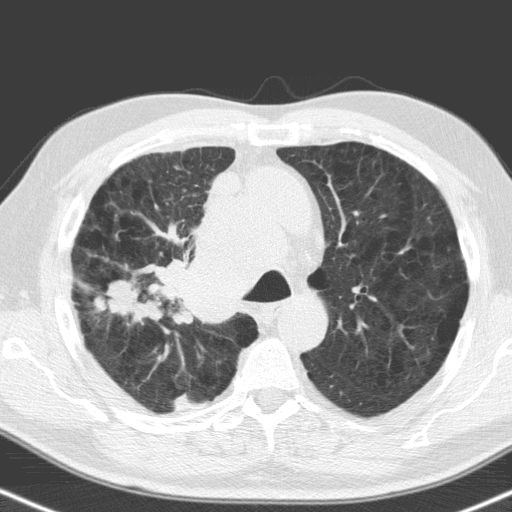
Low-dose screening chest CT, one axial slice; position 116 of 160 along the scan axis; lung window (W 1500 / L -600 HU); 3.2 mm slice thickness; 512 × 512 image matrix, field of view 324 × 324 mm.
Structures marked on this image (outlined manually by an expert reader):
- lesion 1 (tumor, hilum of right lung): bounding box <162,202,248,323> (left, top, right, bottom; pixels)
- lesion 2 (tumor, upper lobe of right lung): <108,281,152,318>